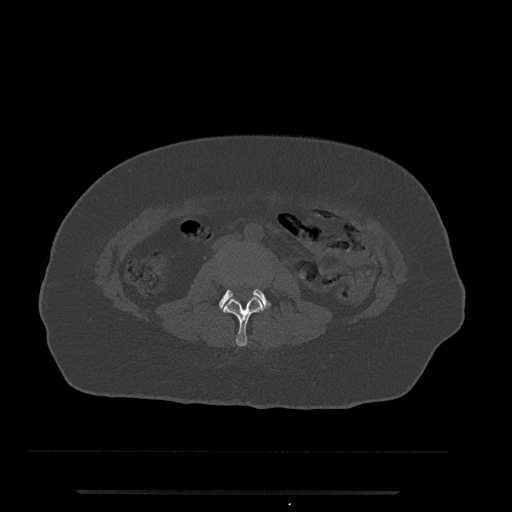
CT including the spine, one axial slice; slice 4 of 797 in the series (ordered by position); reconstruction kernel Br40s/3; 120 kVp; bone window (W 1800 / L 400 HU); 0.5 mm slice thickness; 512 × 512 image matrix, field of view 440 × 440 mm. Female patient, age 51 years. From the clinical record (not read from this slice): primary cancer: neuro; vertebrae with lytic lesions (as recorded): T8.
Annotated regions visible in this slice (semi-automatically segmented with operator editing):
- L2 vertebra: box from (x=222, y=294) to (x=265, y=347) px